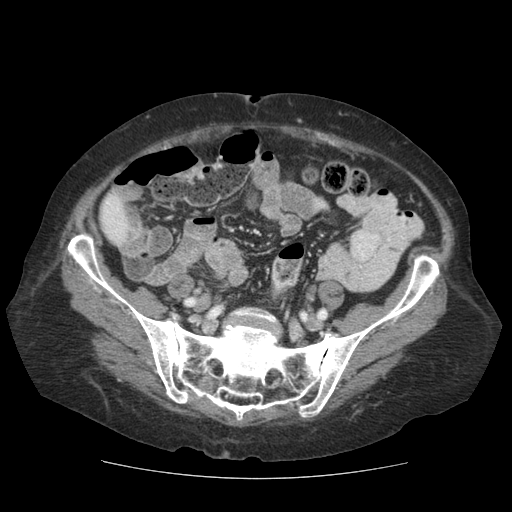
Contrast-enhanced abdominal CT (liver protocol), one axial slice. Position 13 of 111 along the scan axis. Reconstruction kernel STANDARD. Soft-tissue window (W 400 / L 40 HU). 2.5 mm slice thickness. 512 × 512 image matrix, field of view 360 × 360 mm. From the clinical record (not read from this slice): diagnosis: hepatocellular carcinoma (patient treated with transarterial chemoembolisation; whether this scan precedes or follows treatment is not stated here); TNM stage (as recorded): Stage-I; Child-Pugh class: A; tumour differentiation: moderately-poorly differentiated; tumour nodularity: uninodular.
Outlined on this slice (semi-automatically segmented with operator editing):
- liver parenchyma outside the tumour (the mass and vessels are separate outlines, so this box may not span the whole liver): bounding box (x1, y1, x2, y2) in pixels: (100, 194, 142, 249)